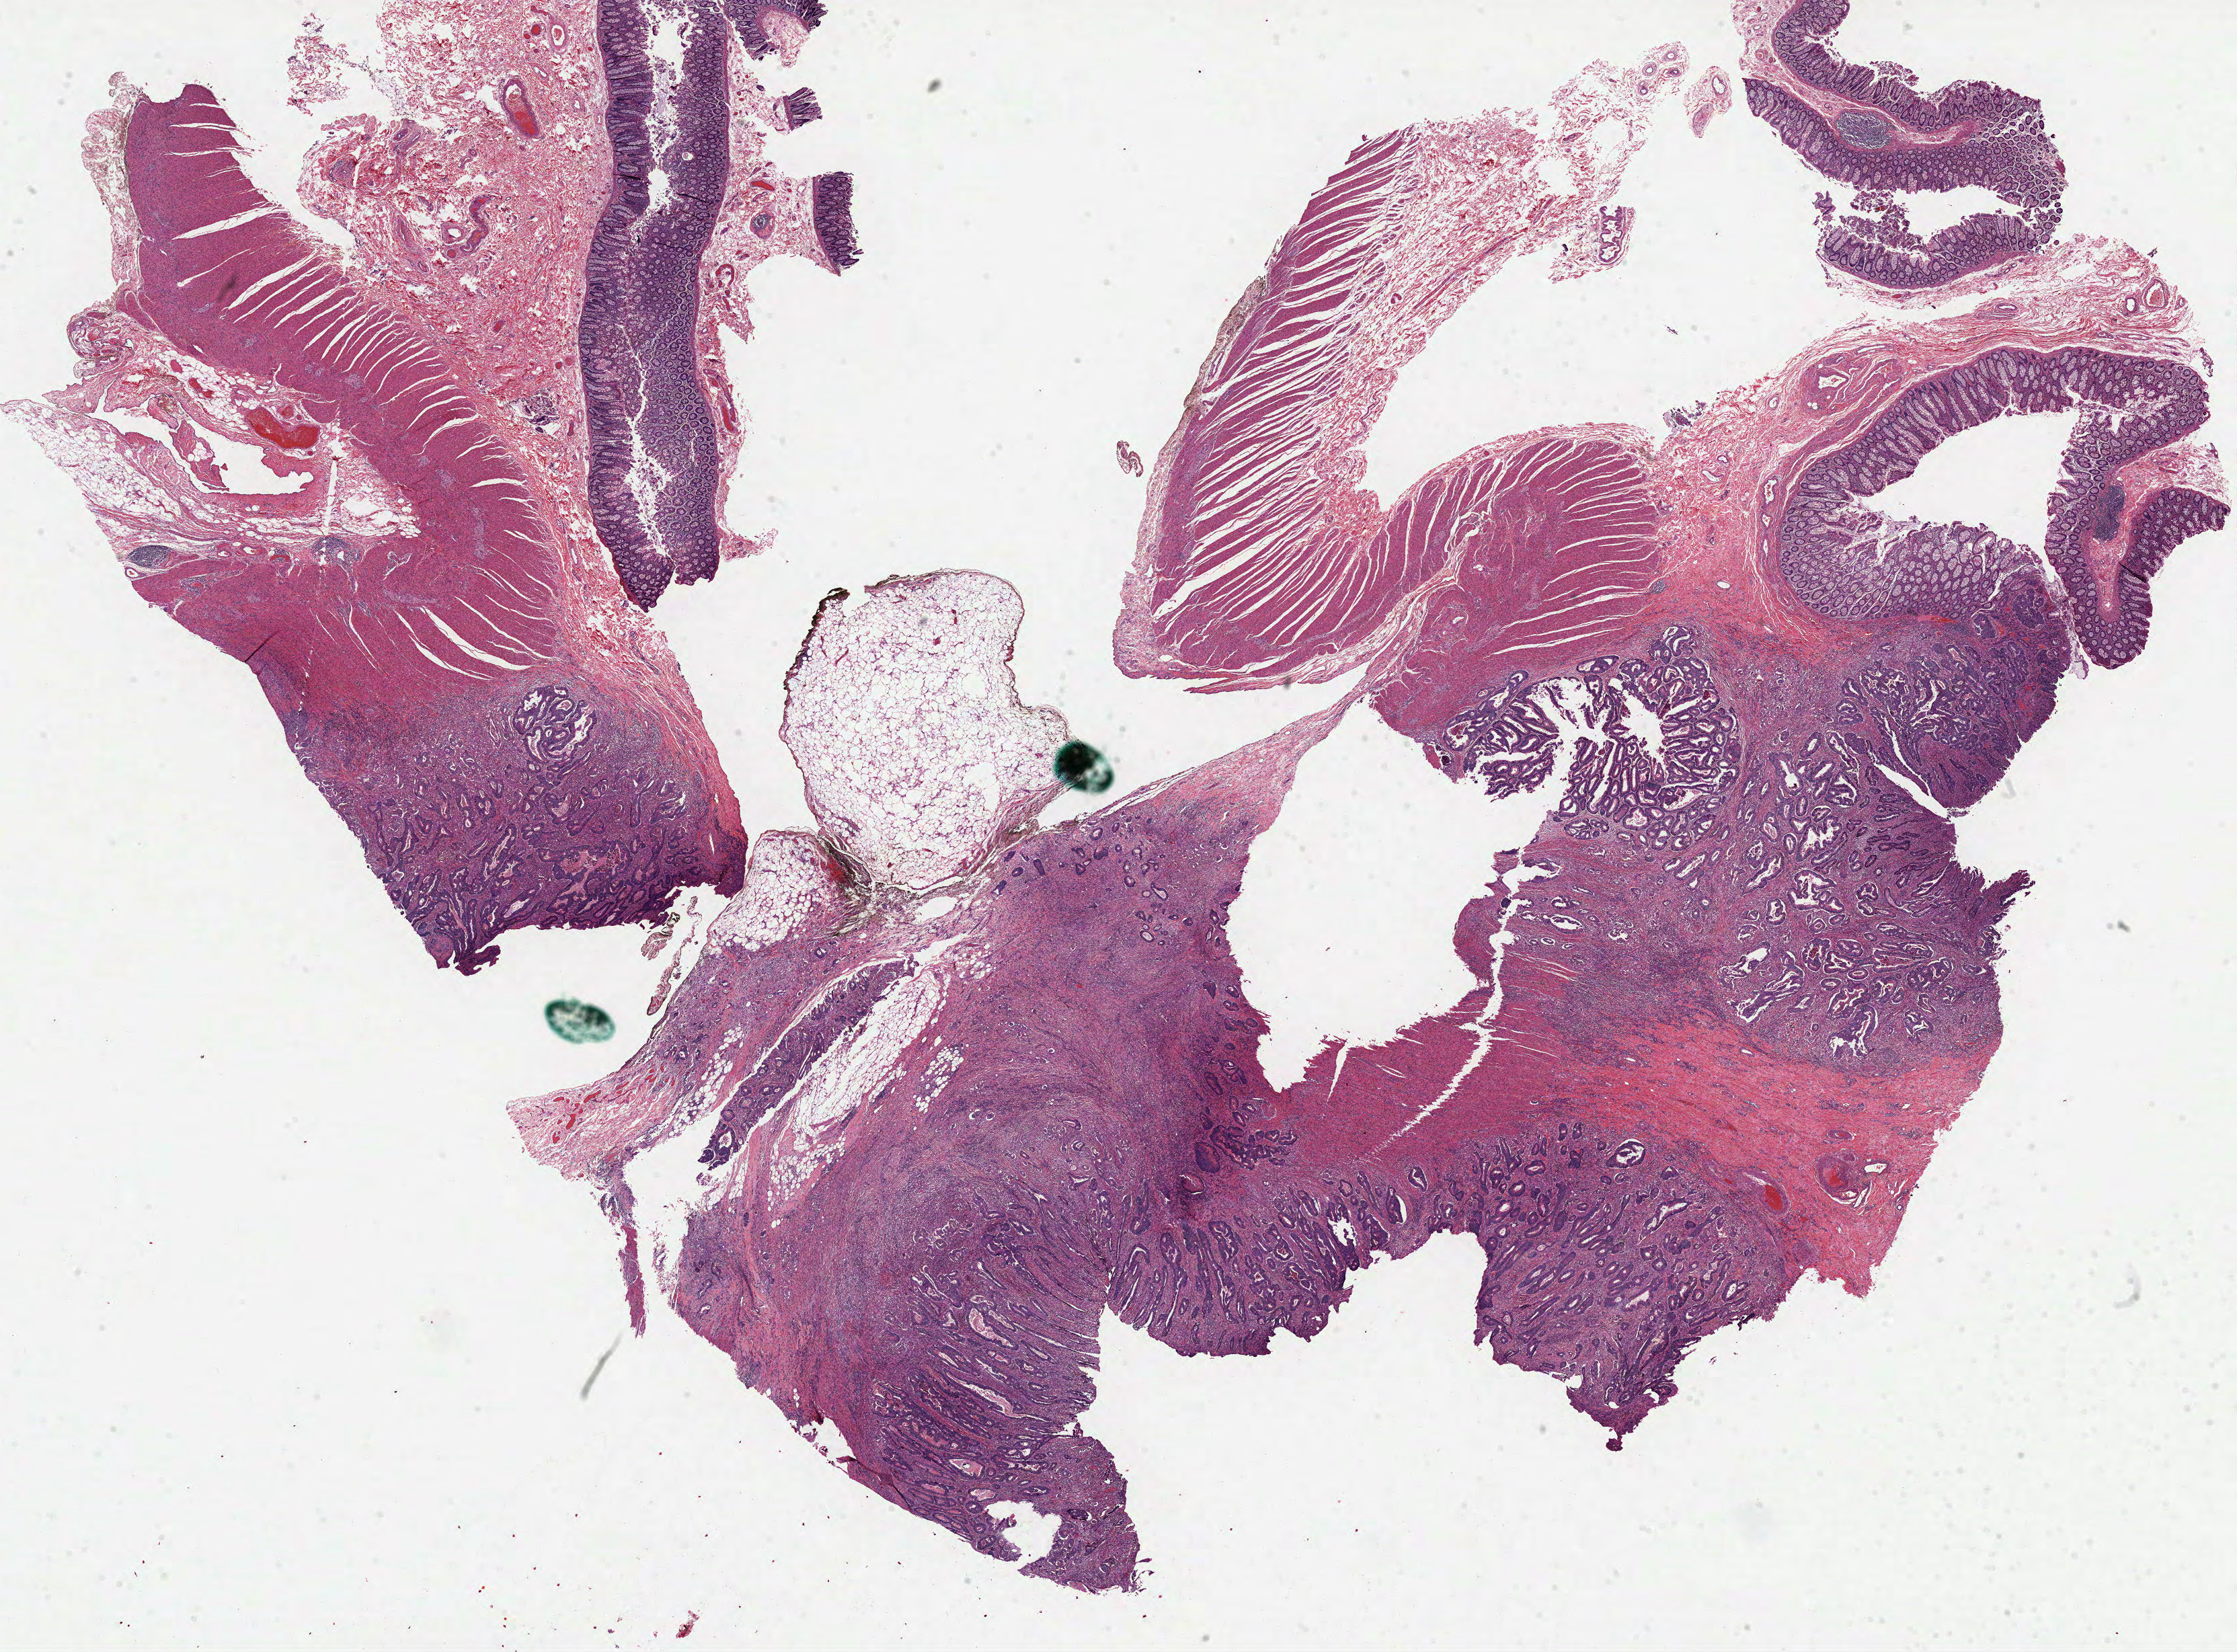
Digitized H&E-stained tissue section (whole slide) — whole scanned area (about 26.8 x 19.8 mm, slide scanned at 40x) shown as a low-resolution overview. Formalin-fixed paraffin-embedded (FFPE) diagnostic section. Sample: primary tumour, colon. Male patient; age at initial diagnosis 77 years.
TNM: T4 N1 M0. Histologic diagnosis: Adenocarcinoma, NOS (ascending colon). AJCC pathologic stage: IIIB (6th edition).